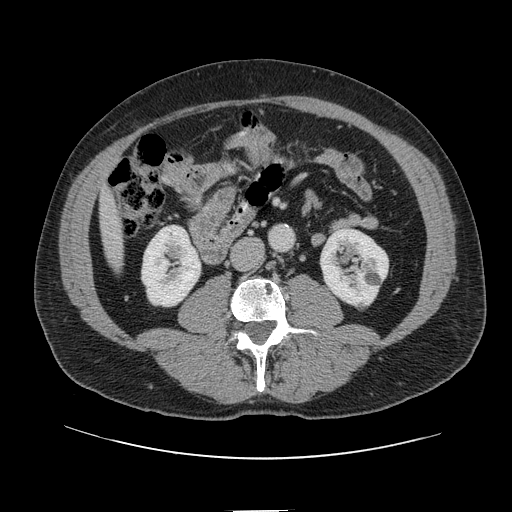
Contrast-enhanced abdominal CT, one axial slice; slice 13 of 161 in the series (ordered by position); intravenous contrast given; soft-tissue window (W 400 / L 40 HU); 512 × 512 image matrix, field of view 412 × 412 mm. Male patient, age 66 years. Case-level facts recorded for this patient, not image findings: diagnosis: colorectal cancer liver metastases, imaged before liver resection; multiple liver metastases: no; largest metastasis: 3.5 cm.
Outlined on this slice (expert manual segmentation):
- liver: bounding box <102,194,122,267> (left, top, right, bottom; pixels)
- planned liver remnant (the part of the liver to remain after resection): <102,193,119,240>